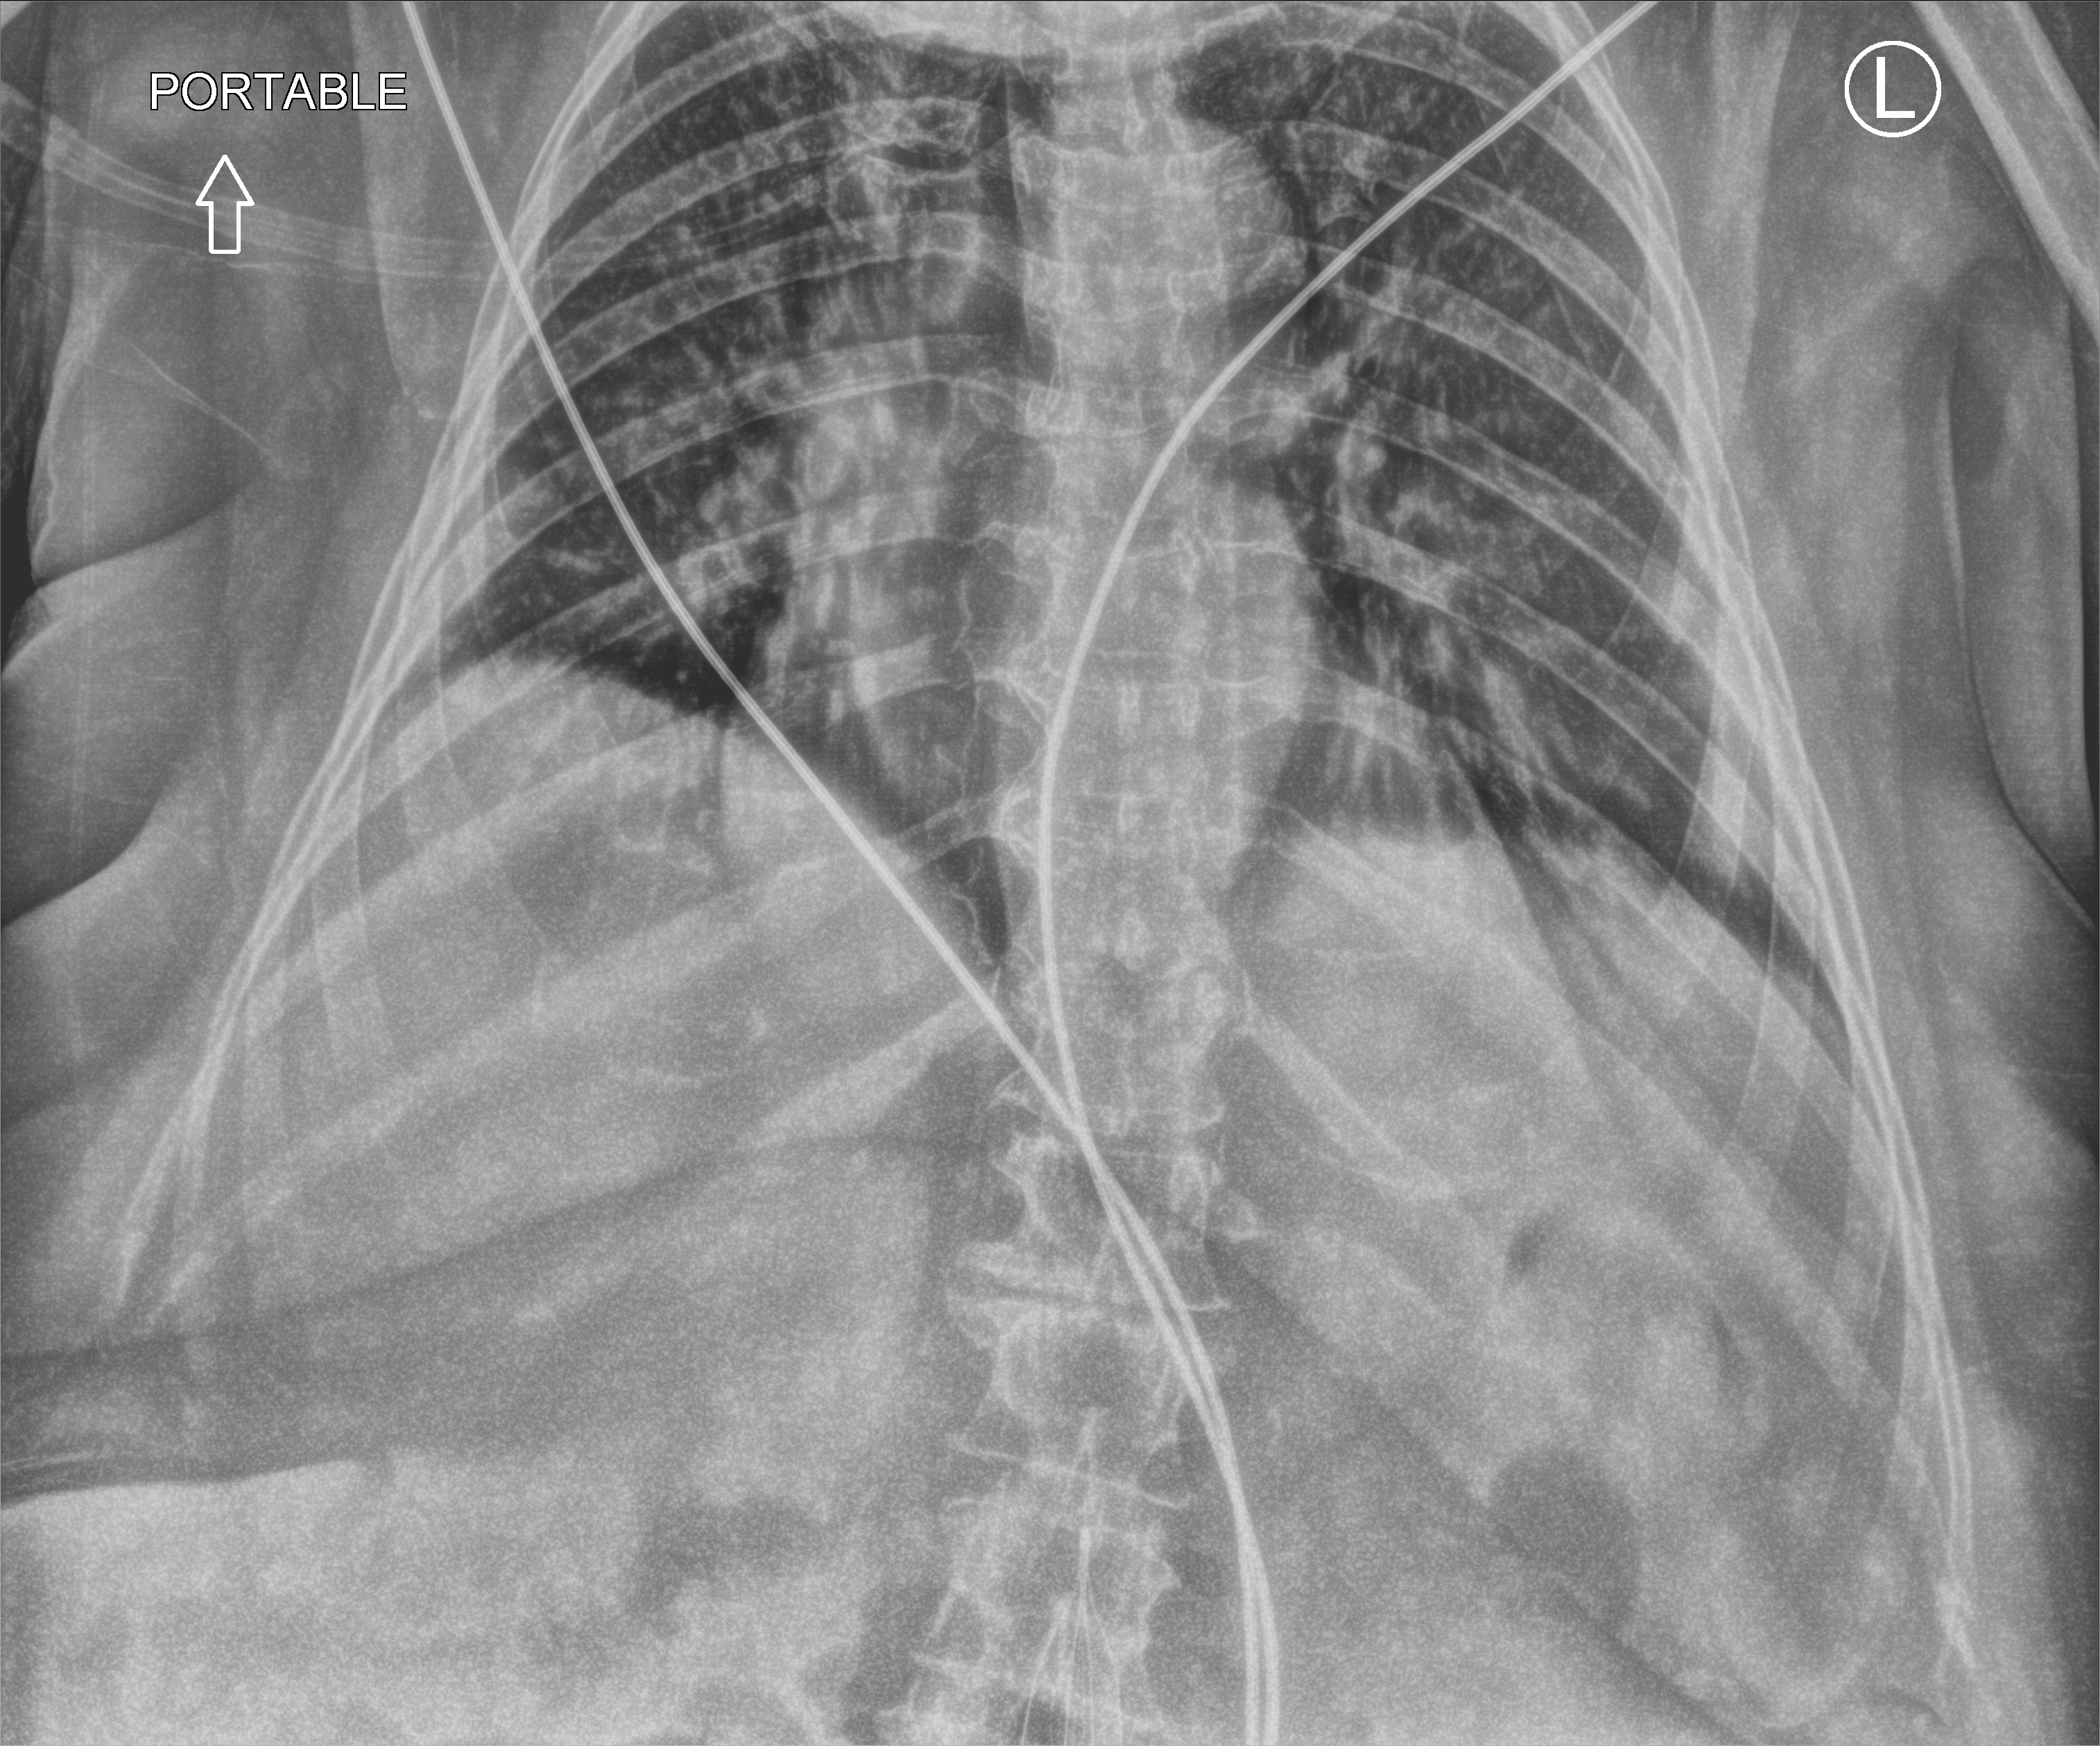
Abdomen X-ray (portable), anteroposterior (AP) projection. Female patient hospitalised with COVID-19, age 60–74 years.
Admission-level facts for this patient (not findings on this image; timing relative to this image not recorded):
- admitted to intensive care during this hospital stay: no